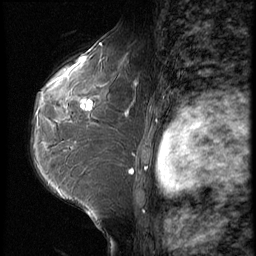
Breast MRI (dynamic contrast-enhanced), one sagittal slice; slice 43 of 62 in the series (ordered by position); 3 images stored at this slice position (order not interpretable as contrast timing); 1.5 T; TE 4.2 ms, TR 9 ms; 2.5 mm slice thickness; 256 × 256 image matrix, field of view 180 × 180 mm. Female patient, age 50 years. Case-level facts recorded for this patient, not image findings: setting: breast cancer imaged before/during neoadjuvant chemotherapy; receptor status: HR-positive, HER2-negative.
Annotated regions visible in this slice (semi-automatic segmentation, software-assisted and operator-edited):
- analysis volume of interest (the breast-tissue region the enhancement analysis was run in; not a lesion): box from (x=32, y=91) to (x=118, y=209) px
- tumour enhancement mask (voxels above the 140 % enhancement threshold inside the analysis volume of interest): (x=82, y=105)–(x=91, y=108)